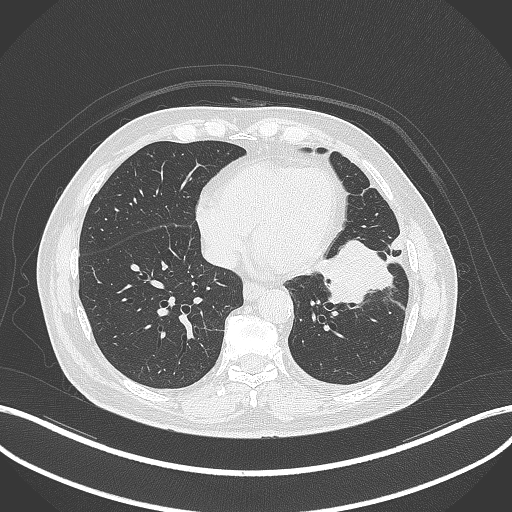
Chest CT, one axial slice; slice 122 of 230 in the series (ordered by position); reconstruction kernel B70f; 120 kVp; lung window (W 1500 / L -600 HU); 1 mm slice thickness; 512 × 512 image matrix, field of view 400 × 400 mm. Male patient, age 68 years. Case-level facts recorded for this patient, not image findings: clinical TNM (as recorded): T2b N0 M0.
Outlined on this slice (bounding box drawn by a radiologist):
- lung tumour (recorded histology: squamous cell carcinoma): bounding box [x1, y1, x2, y2] px = [317, 242, 395, 313]